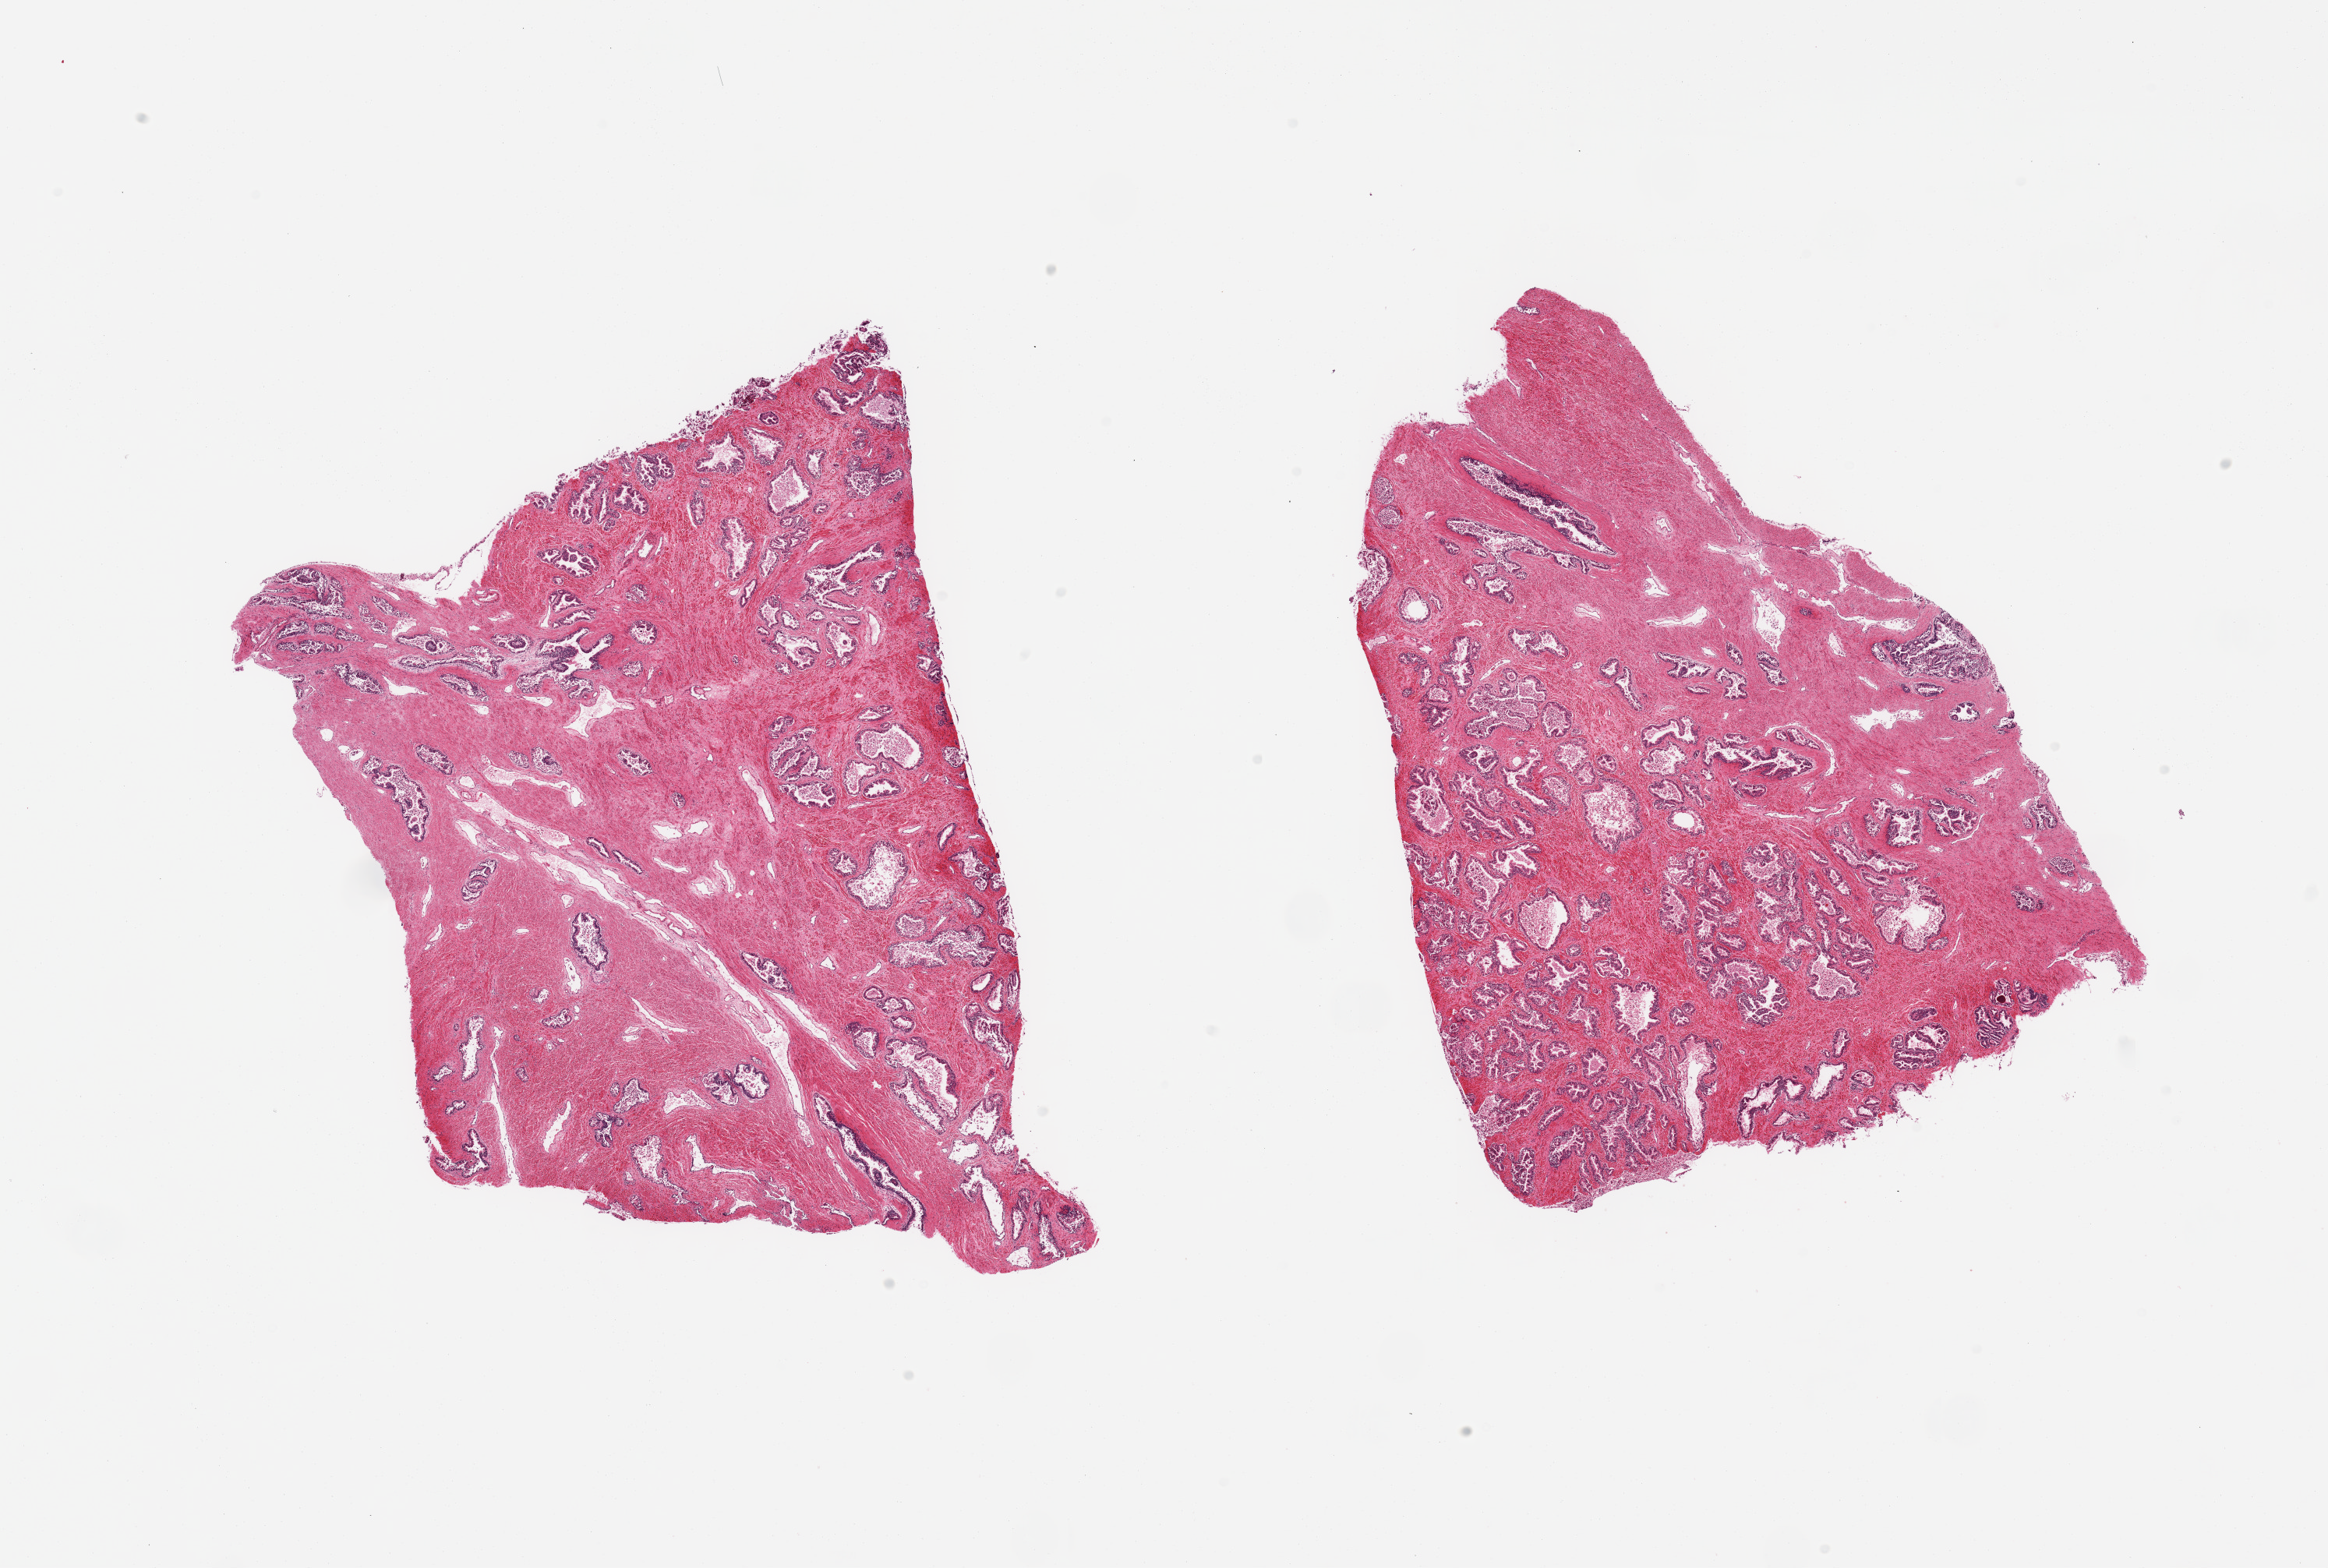
Digitized hematoxylin and eosin (H&E)-stained section — whole scanned area (about 23.6 x 15.9 mm, acquisition: 20x scan) shown as a low-resolution overview. PAXgene-fixed paraffin-embedded (PFPE) section. Sampled site (target tissue): prostate. Tissue donor sample.
• pathologist's review note for this sample: 2 pieces; mild to moderate autolysis; fibromuscular stroma and glandular component with focally sloughed epithelium